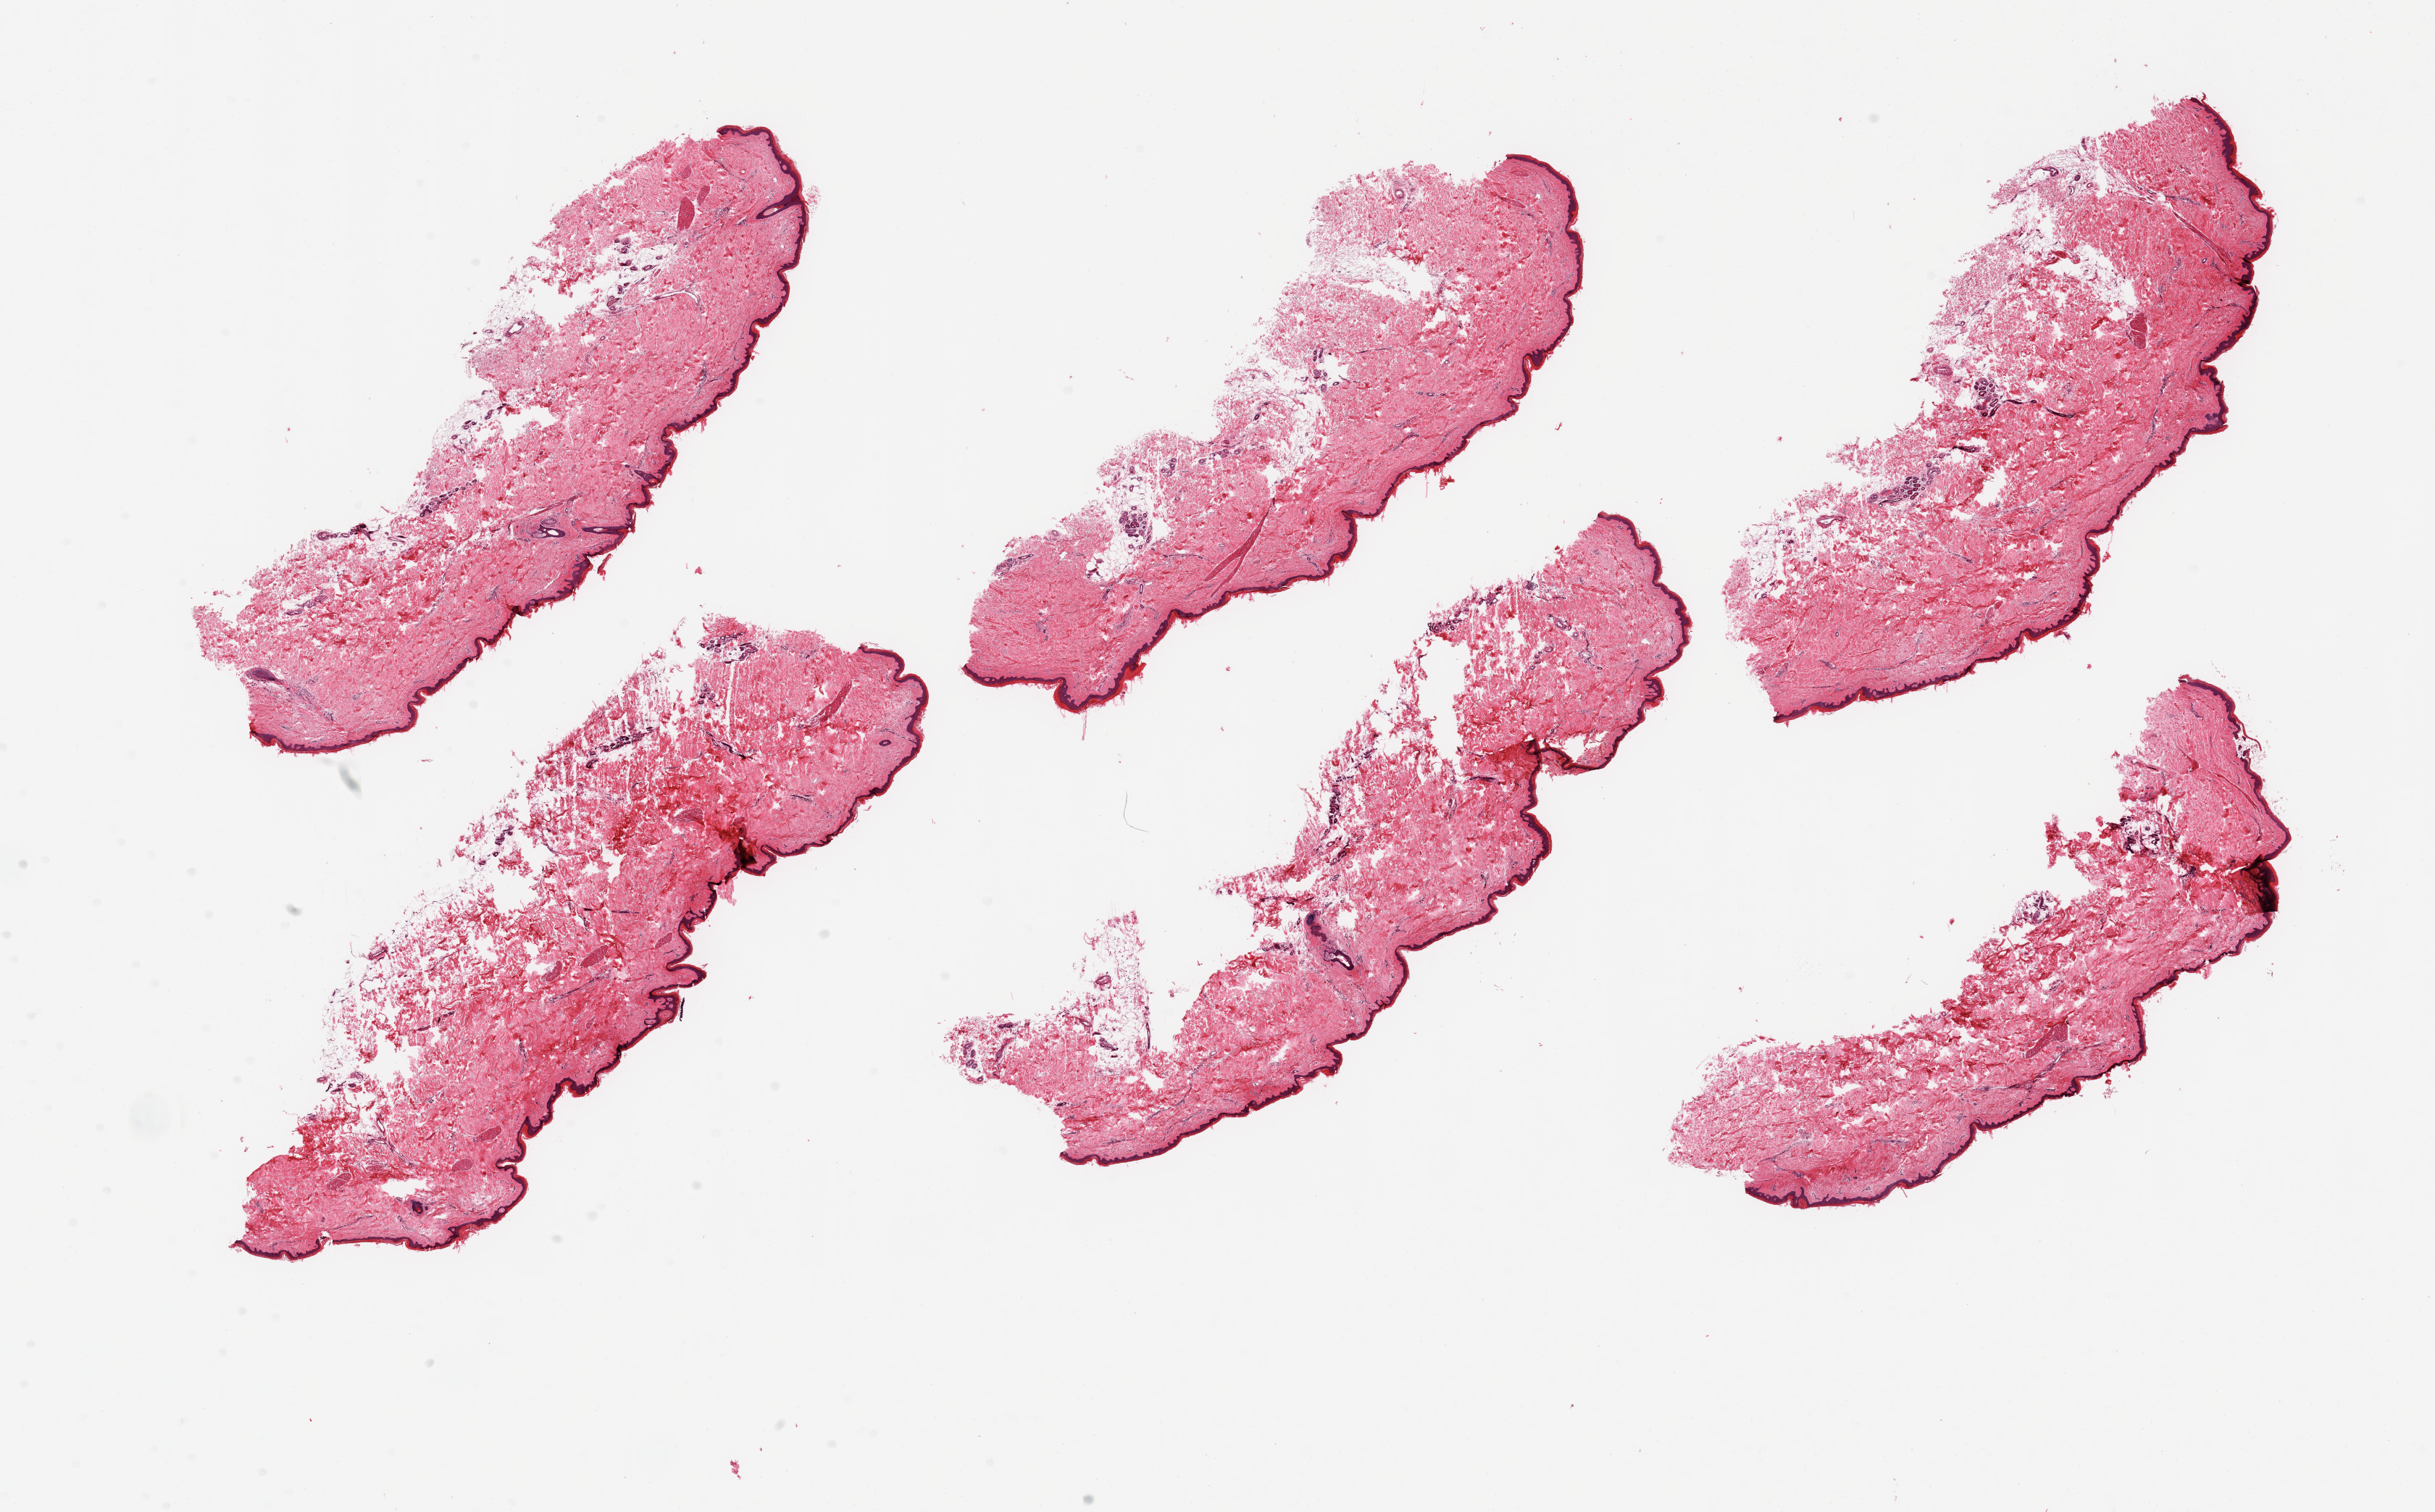
Haematoxylin and eosin whole-slide image, shown as a low-resolution overview of the whole scanned area (about 26.6 x 16.5 mm, acquisition: 20x scan); PAXgene-fixed, paraffin-embedded tissue; sampled site (target tissue): skin of lower leg; tissue donor sample.
* review note (as recorded): 6 pieces; ~40 microns thick epidermis; ~20% internal fat; well trimmed